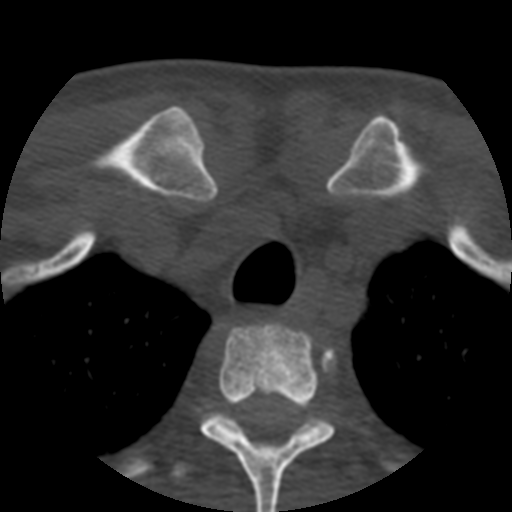
CT including the spine, one axial slice. Position 428 of 508 along the scan axis. Bone window (W 1800 / L 400 HU). 1.25 mm slice thickness. 512 × 512 image matrix, field of view 160 × 160 mm. Patient age 57 years. From the clinical record (not read from this slice): primary cancer: prostate.
Outlined on this slice (semi-automatically segmented with operator editing):
- T2 vertebra: bounding box [x1, y1, x2, y2] px = [200, 323, 335, 512]
- T3 vertebra: [172, 420, 334, 477]